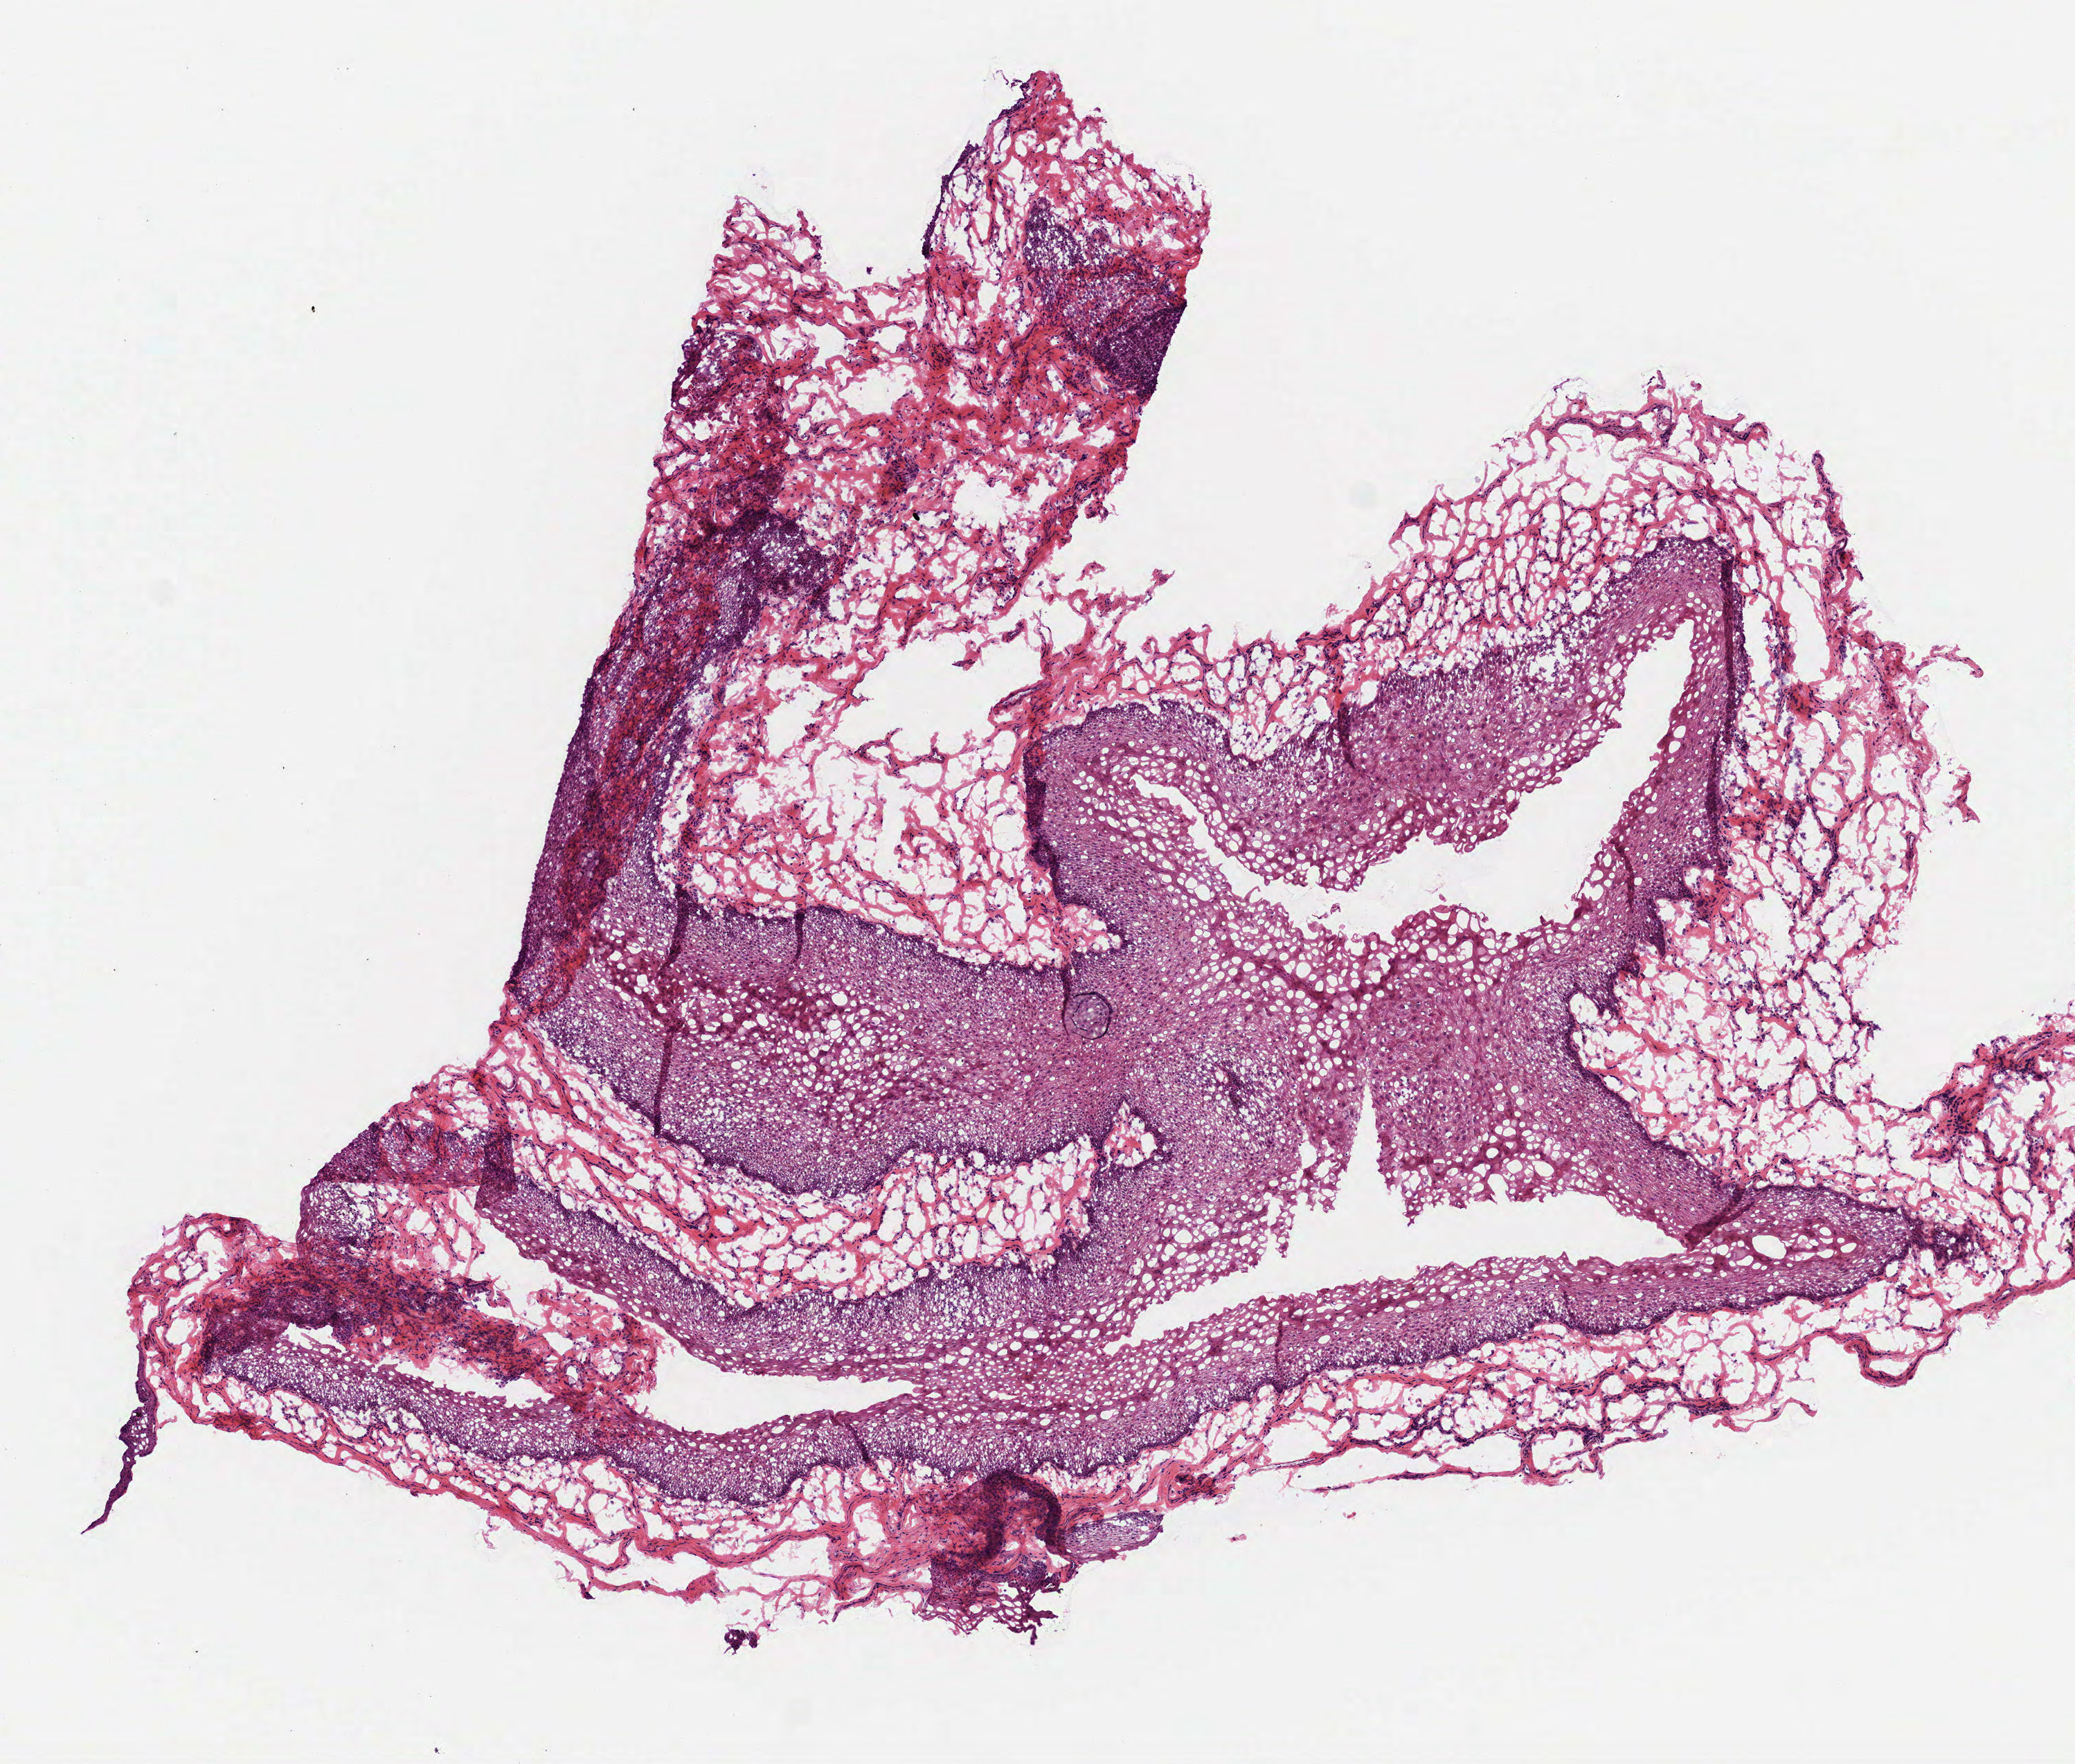
Hematoxylin and eosin (H&E) stained whole-slide image — shown as a low-resolution overview of the whole scanned area (about 6.0 x 5.1 mm, from a 40x scan); frozen section from the top of the tissue portion; sample: solid tissue normal (non-tumour tissue), head and neck. Male patient; age at initial diagnosis 55 years.
This section: solid tissue normal sample (biorepository sample class). Patient diagnosis: Squamous cell carcinoma, NOS (larynx, NOS).